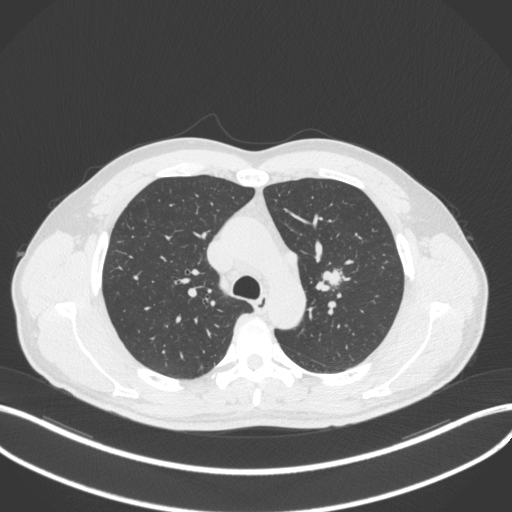
Chest CT, one axial slice; slice 300 of 383 in the series (ordered by position); 120 kVp; lung window (W 1500 / L -600 HU); 1 mm slice thickness; 512 × 512 image matrix. Male patient, age 50 years. From the clinical record (not read from this slice): clinical TNM (as recorded): T1c N1 M1b.
Outlined on this slice (bounding box drawn by a radiologist):
- lung tumour (recorded histology: squamous cell carcinoma): bounding box <314,264,343,292> (left, top, right, bottom; pixels)